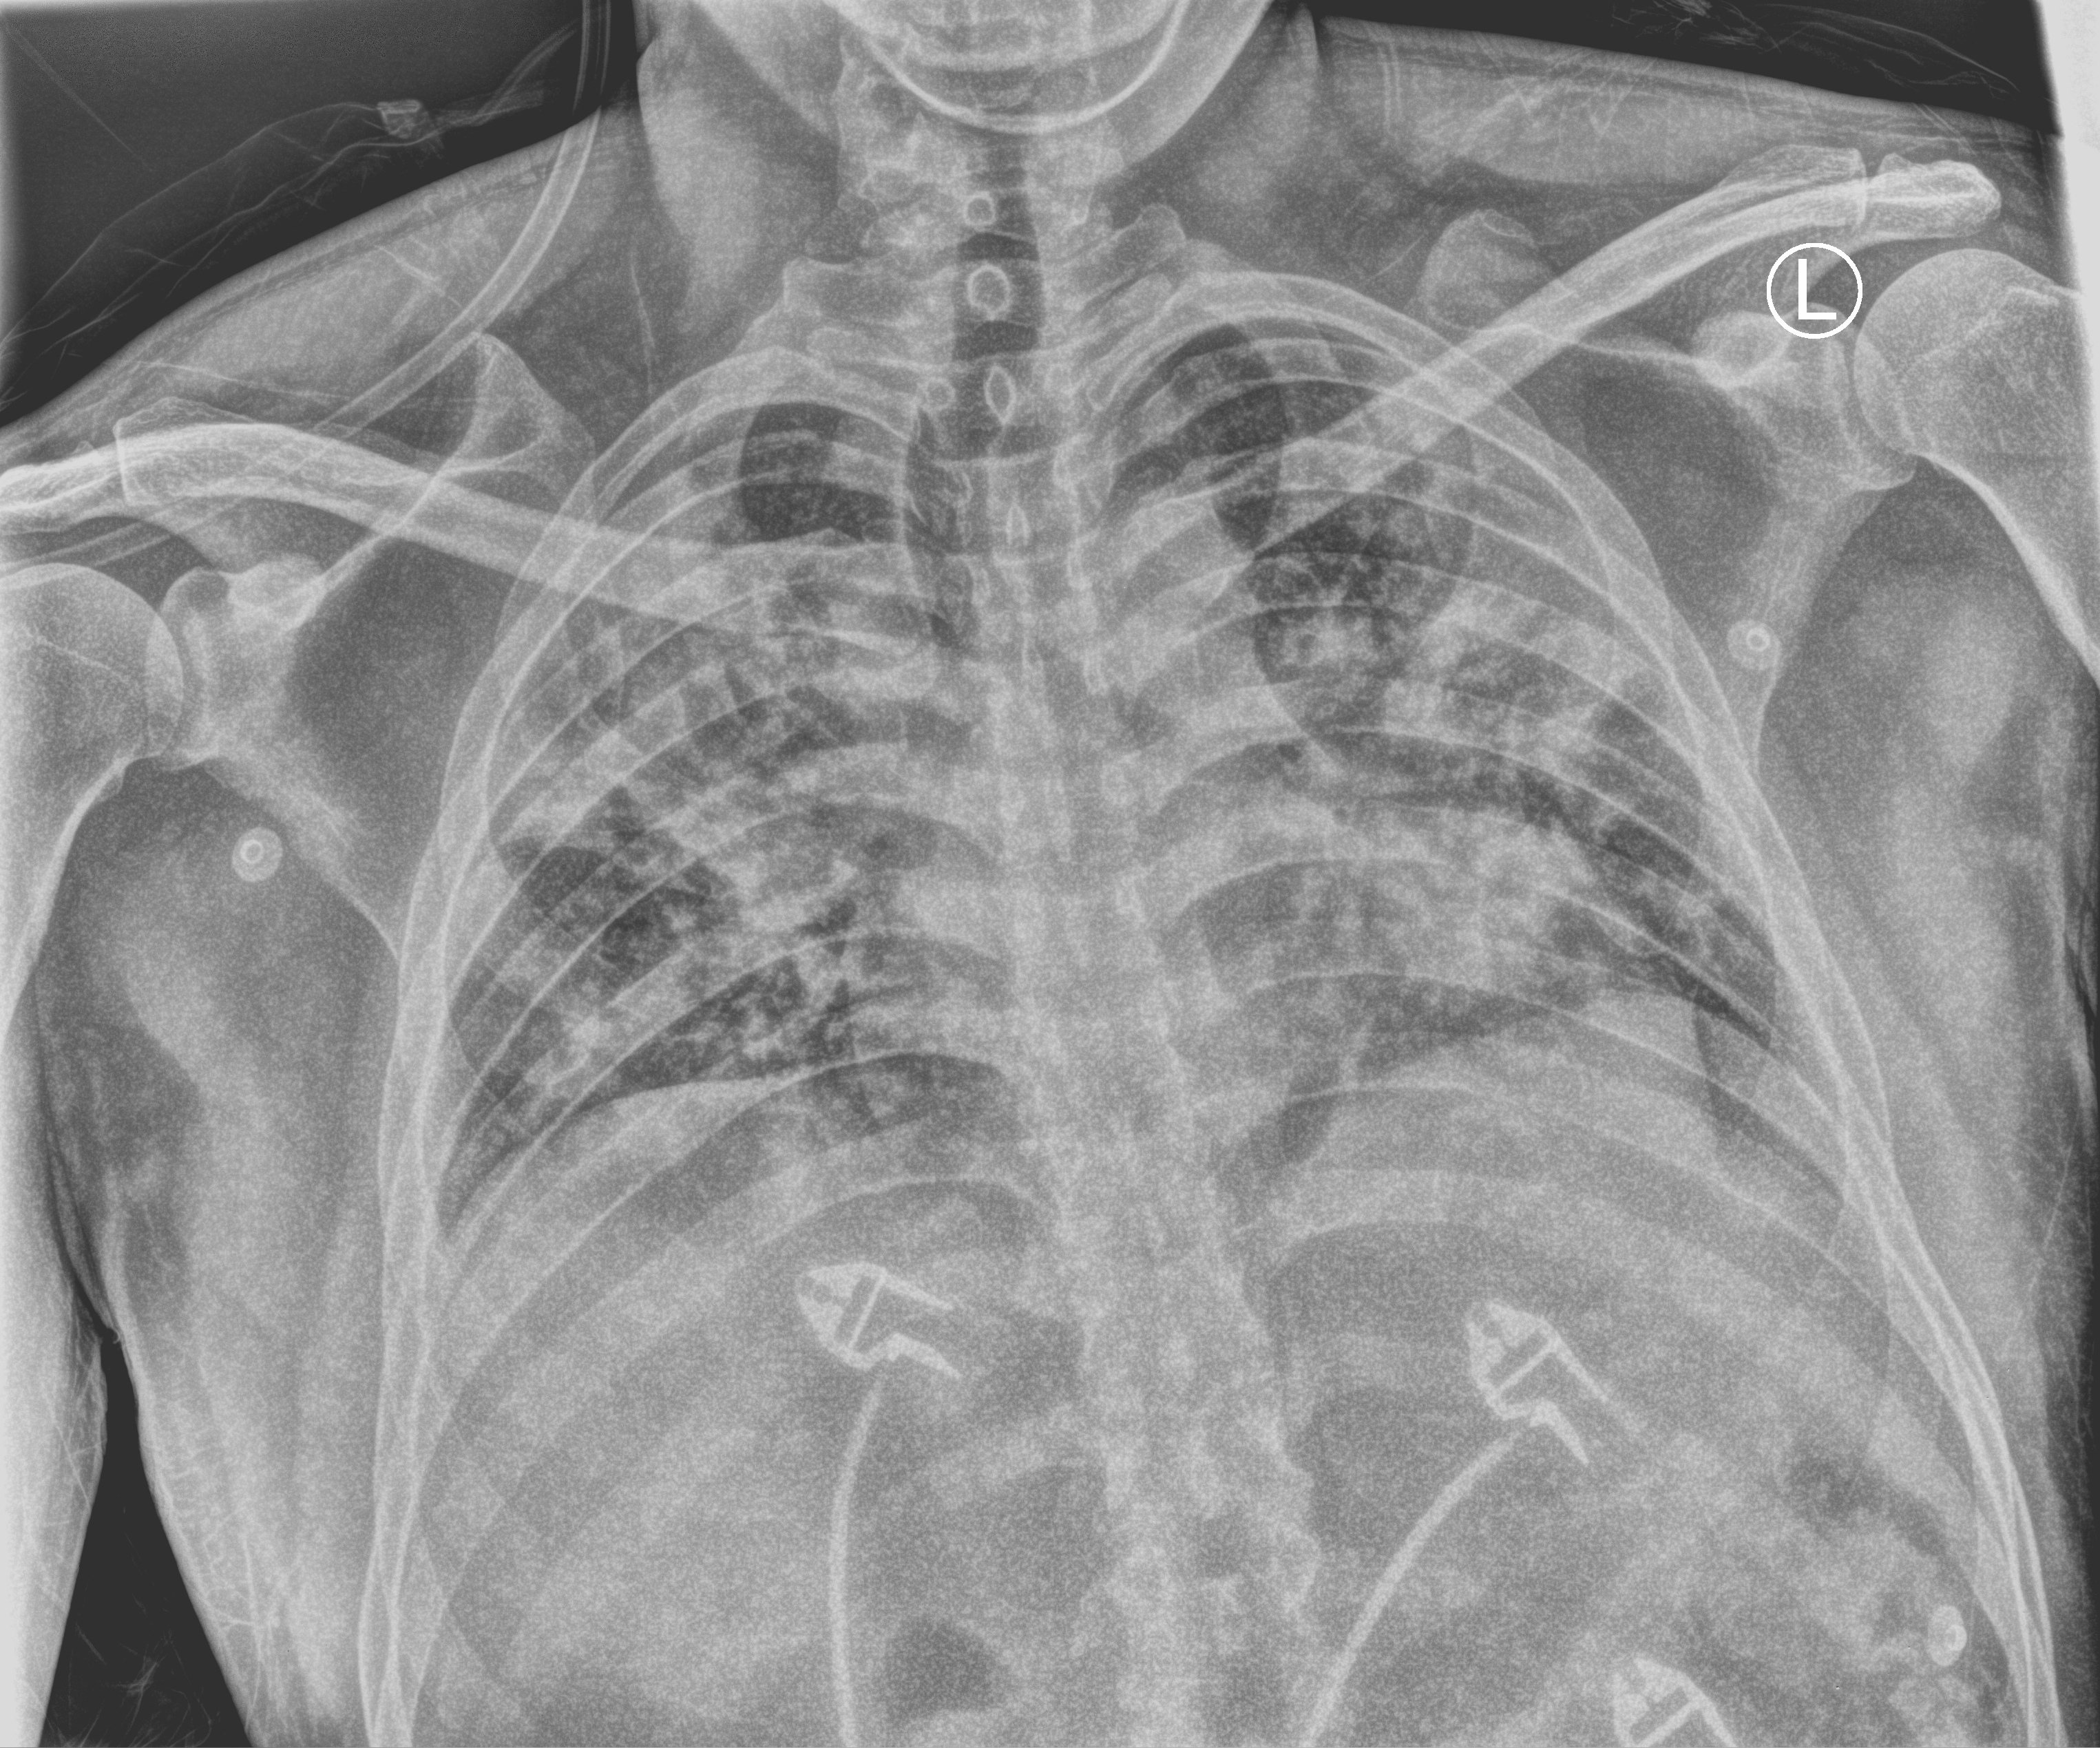
Portable chest radiograph; anteroposterior (AP) projection. Male patient hospitalised with COVID-19, age 18–59 years.
Hospital-stay facts (about this admission, not read from this image; timing relative to this image not recorded): other chronic lung disease (admission record): no.